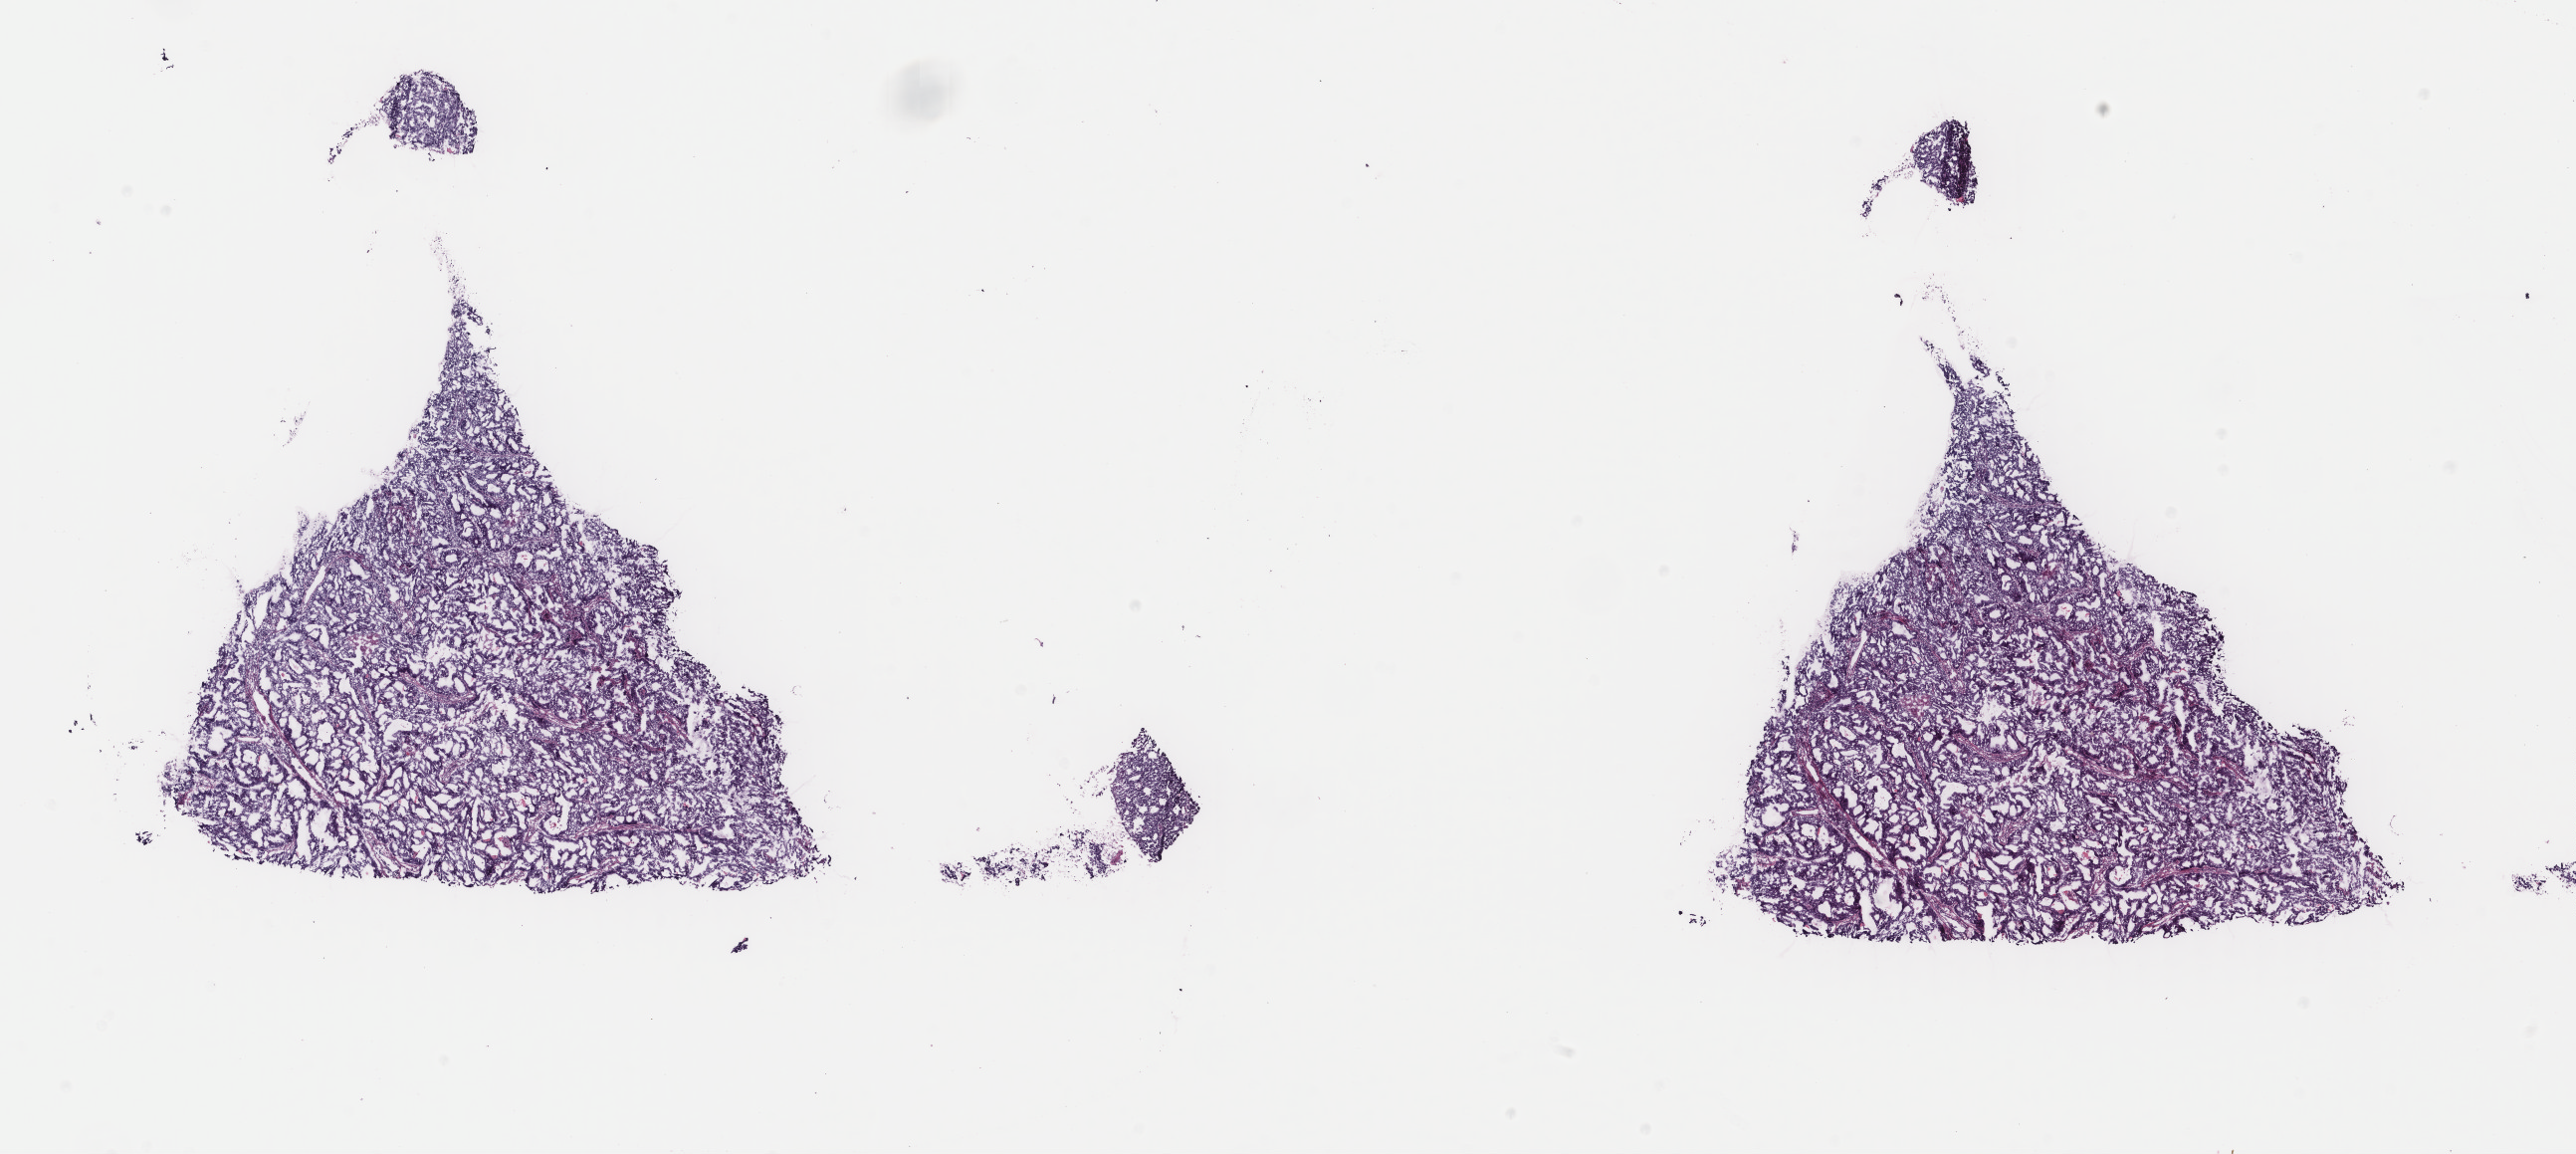
Digitized Hematoxylin and eosin (H&E) stained tissue section (whole slide), whole scanned area (about 20.5 x 9.2 mm, from a 40x scan) shown as a low-resolution overview. Frozen section from the top of the tissue portion. Primary tumour sample from the uterus. Female patient; age at initial diagnosis 58 years. Histologic grade: G2 (moderately differentiated). Composition of this section per pathologist review: tumour cells 89%, tumour nuclei 85%, normal cells 1%, stromal cells 8%, necrosis 2%. Inflammatory infiltration, as recorded: lymphocyte infiltration 8%, monocyte infiltration 1%, neutrophil infiltration 1%.
• FIGO stage: IB
• pathologic diagnosis: Endometrioid adenocarcinoma, NOS (endometrium)